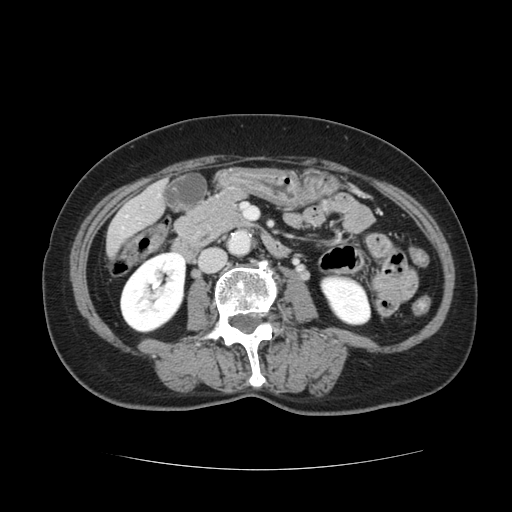
Contrast-enhanced abdominal CT, one axial slice. Slice 25 of 128 in the series (ordered by position). Soft-tissue window (W 400 / L 40 HU). 2.5 mm slice thickness. 512 × 512 image matrix. Female patient, age 67 years. From the clinical record (not read from this slice): diagnosis: colorectal cancer liver metastases, imaged before liver resection; multiple liver metastases: yes; largest metastasis: 3 cm; chemotherapy before resection: no.
Structures marked on this image (manually delineated by an expert):
- liver: bounding box (x1, y1, x2, y2) in pixels: (108, 184, 165, 252)
- planned liver remnant (the part of the liver to remain after resection): (108, 209, 140, 252)